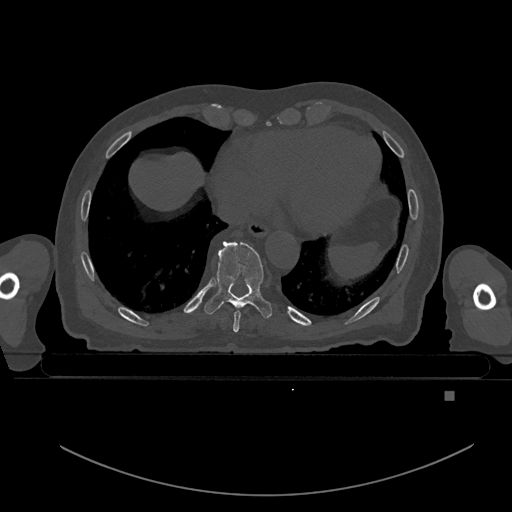
CT including the spine, one axial slice; position 156 of 969 along the scan axis; bone window (W 1800 / L 400 HU); 0.5 mm slice thickness; 512 × 512 image matrix, field of view 456 × 456 mm. Patient: male, 82 years. Case-level facts recorded for this patient, not image findings: primary cancer: prostate; vertebrae with lytic lesions (as recorded): T11, T9, T8, T2.
Structures marked on this image (semi-automatically segmented with operator editing):
- T8 vertebra: bounding box [x1, y1, x2, y2] px = [233, 311, 241, 333]
- T9 vertebra: [204, 241, 272, 319]